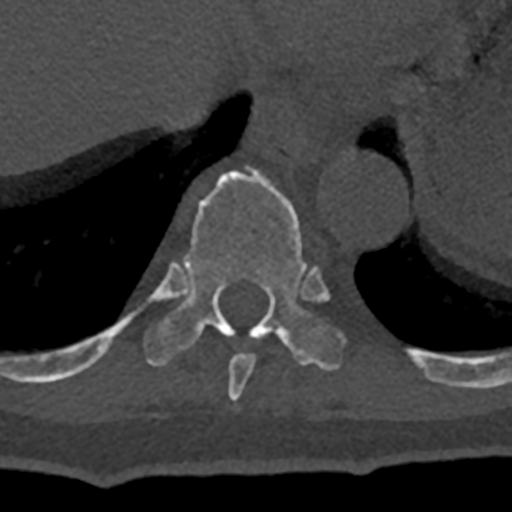
CT including the spine, one axial slice; slice 615 of 797 in the series (ordered by position); reconstruction kernel Br40s/3; bone window (W 1800 / L 400 HU); 0.5 mm slice thickness; 512 × 512 image matrix, field of view 160 × 160 mm. Male patient, age 74 years. Case-level facts recorded for this patient, not image findings: primary cancer: renal; vertebrae with lytic lesions (as recorded): T10, L1, L2, L3, L4, L5.
Annotated regions visible in this slice (semi-automatically segmented with operator editing):
- T10 vertebra: box from (x=70, y=166) to (x=432, y=380) px
- T9 vertebra: (x=228, y=353)–(x=256, y=401)